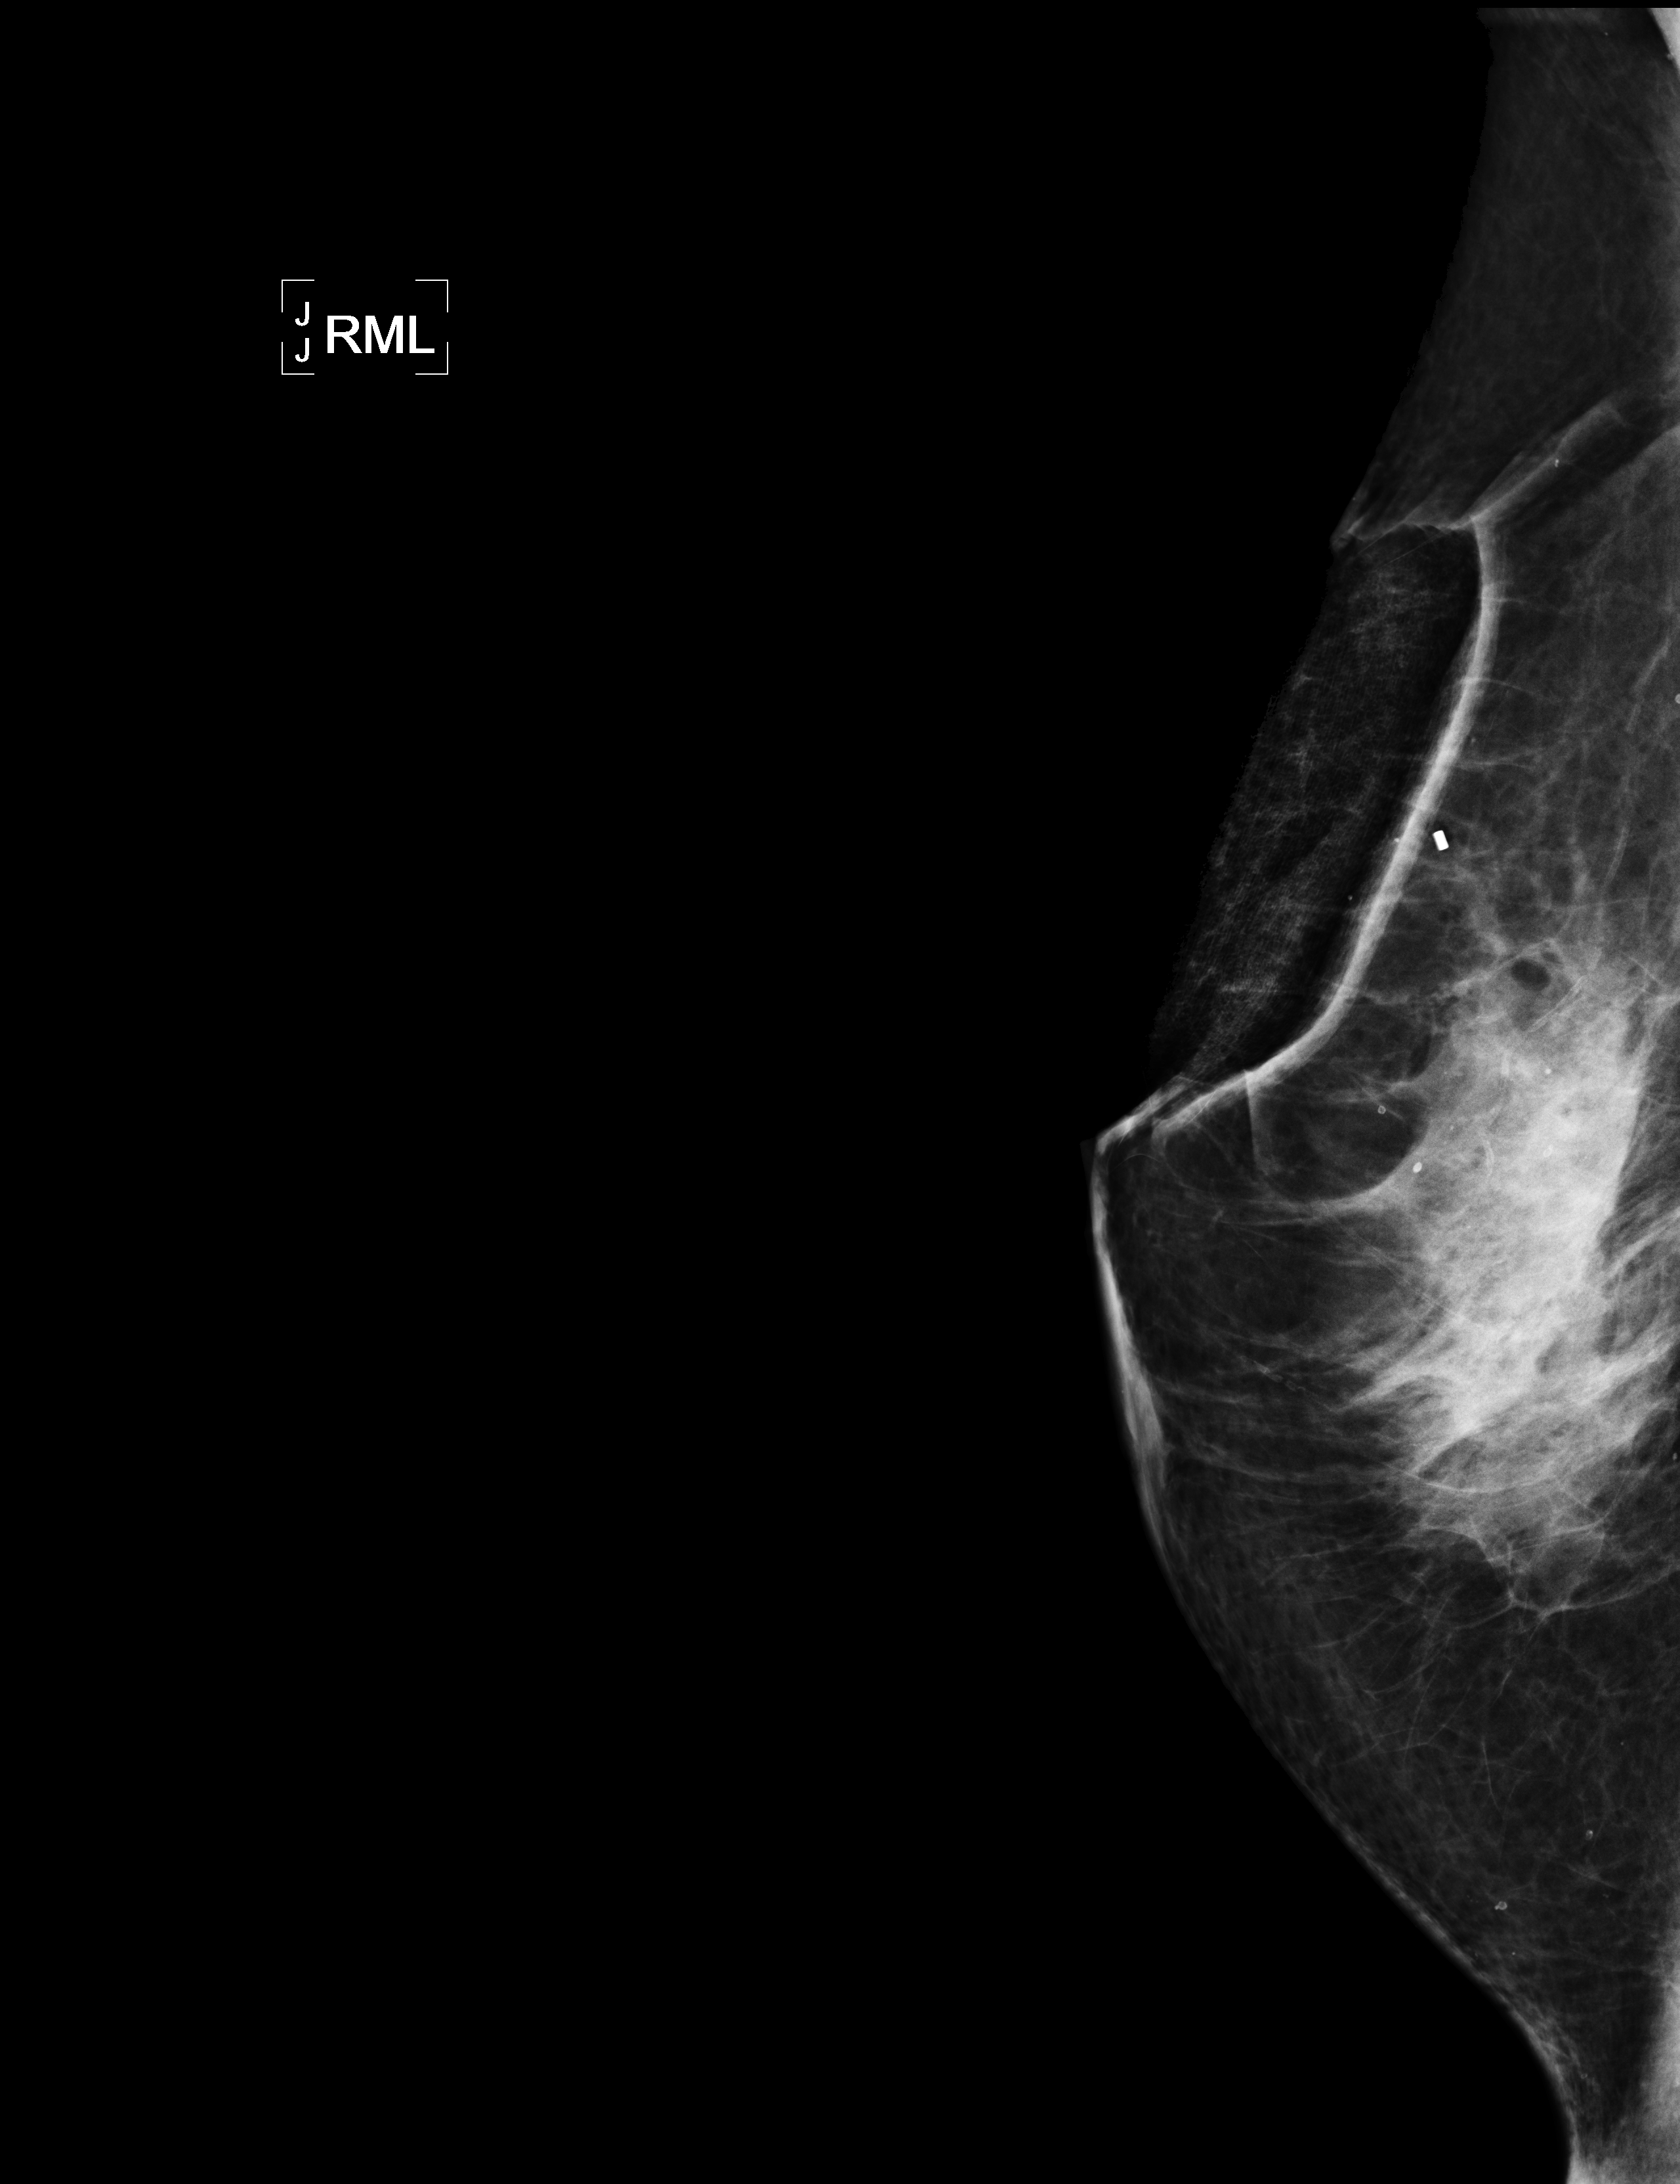
Diagnostic work-up study, system: Lorad Selenia. Patient aged 68 years (female).
Image type: full-field digital mammogram. Breast: right. Projection: mediolateral (ML) view.